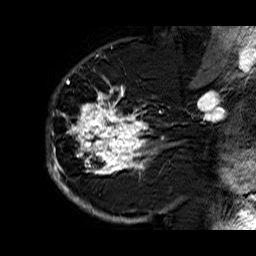
Breast MRI (dynamic contrast-enhanced), one sagittal slice. Slice 43 of 60 in the series (ordered by position). Dynamic contrast-enhanced series, time point 2 of 6 at this slice position (early post-contrast). 1.5 T. TE 6.3 ms, TR 32.9 ms. 4 mm slice thickness. 256 × 256 image matrix. Female patient. From the clinical record (not read from this slice): setting: breast cancer imaged before/during neoadjuvant chemotherapy; receptor status: HR-positive, HER2-negative.
Annotated regions visible in this slice (semi-automatic segmentation, software-assisted and operator-edited):
- analysis volume of interest (the breast-tissue region the enhancement analysis was run in; not a lesion): bounding box [x1, y1, x2, y2] px = [46, 74, 176, 210]
- tumour enhancement mask (voxels above the 100 % enhancement threshold inside the analysis volume of interest): [47, 74, 167, 210]